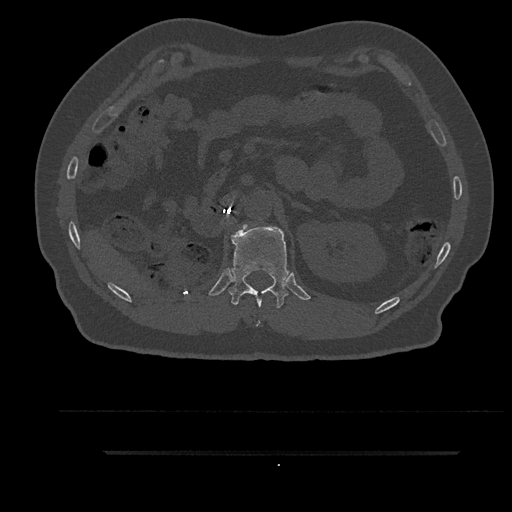
CT including the spine, one axial slice; position 240 of 797 along the scan axis; reconstruction kernel Br40s/3; 120 kVp; bone window (W 1800 / L 400 HU); 512 × 512 image matrix, field of view 432 × 432 mm. Male patient, age 63 years. Case-level facts recorded for this patient, not image findings: primary cancer: renal; vertebrae with lytic lesions (as recorded): T8.
Outlined on this slice (semi-automatically segmented with operator editing):
- T12 vertebra: bounding box (x1, y1, x2, y2) in pixels: (229, 224, 289, 324)